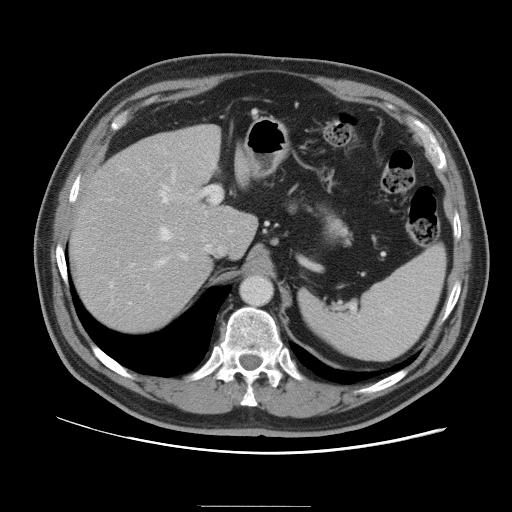
Contrast-enhanced abdominal CT, one axial slice; position 70 of 105 along the scan axis; 120 kVp; intravenous contrast given; soft-tissue window (W 400 / L 40 HU); 512 × 512 image matrix, field of view 399 × 399 mm. Male patient, age 64 years. Case-level facts recorded for this patient, not image findings: diagnosis: colorectal cancer liver metastases, imaged before liver resection; multiple liver metastases: yes; largest metastasis: 3 cm.
Annotated regions visible in this slice (outlined manually by an expert reader):
- hepatic veins: bounding box <158,174,181,265> (left, top, right, bottom; pixels)
- liver: <71,126,255,331>
- planned liver remnant (the part of the liver to remain after resection): <71,140,256,331>
- portal vein (with intrahepatic branches): <110,186,221,288>